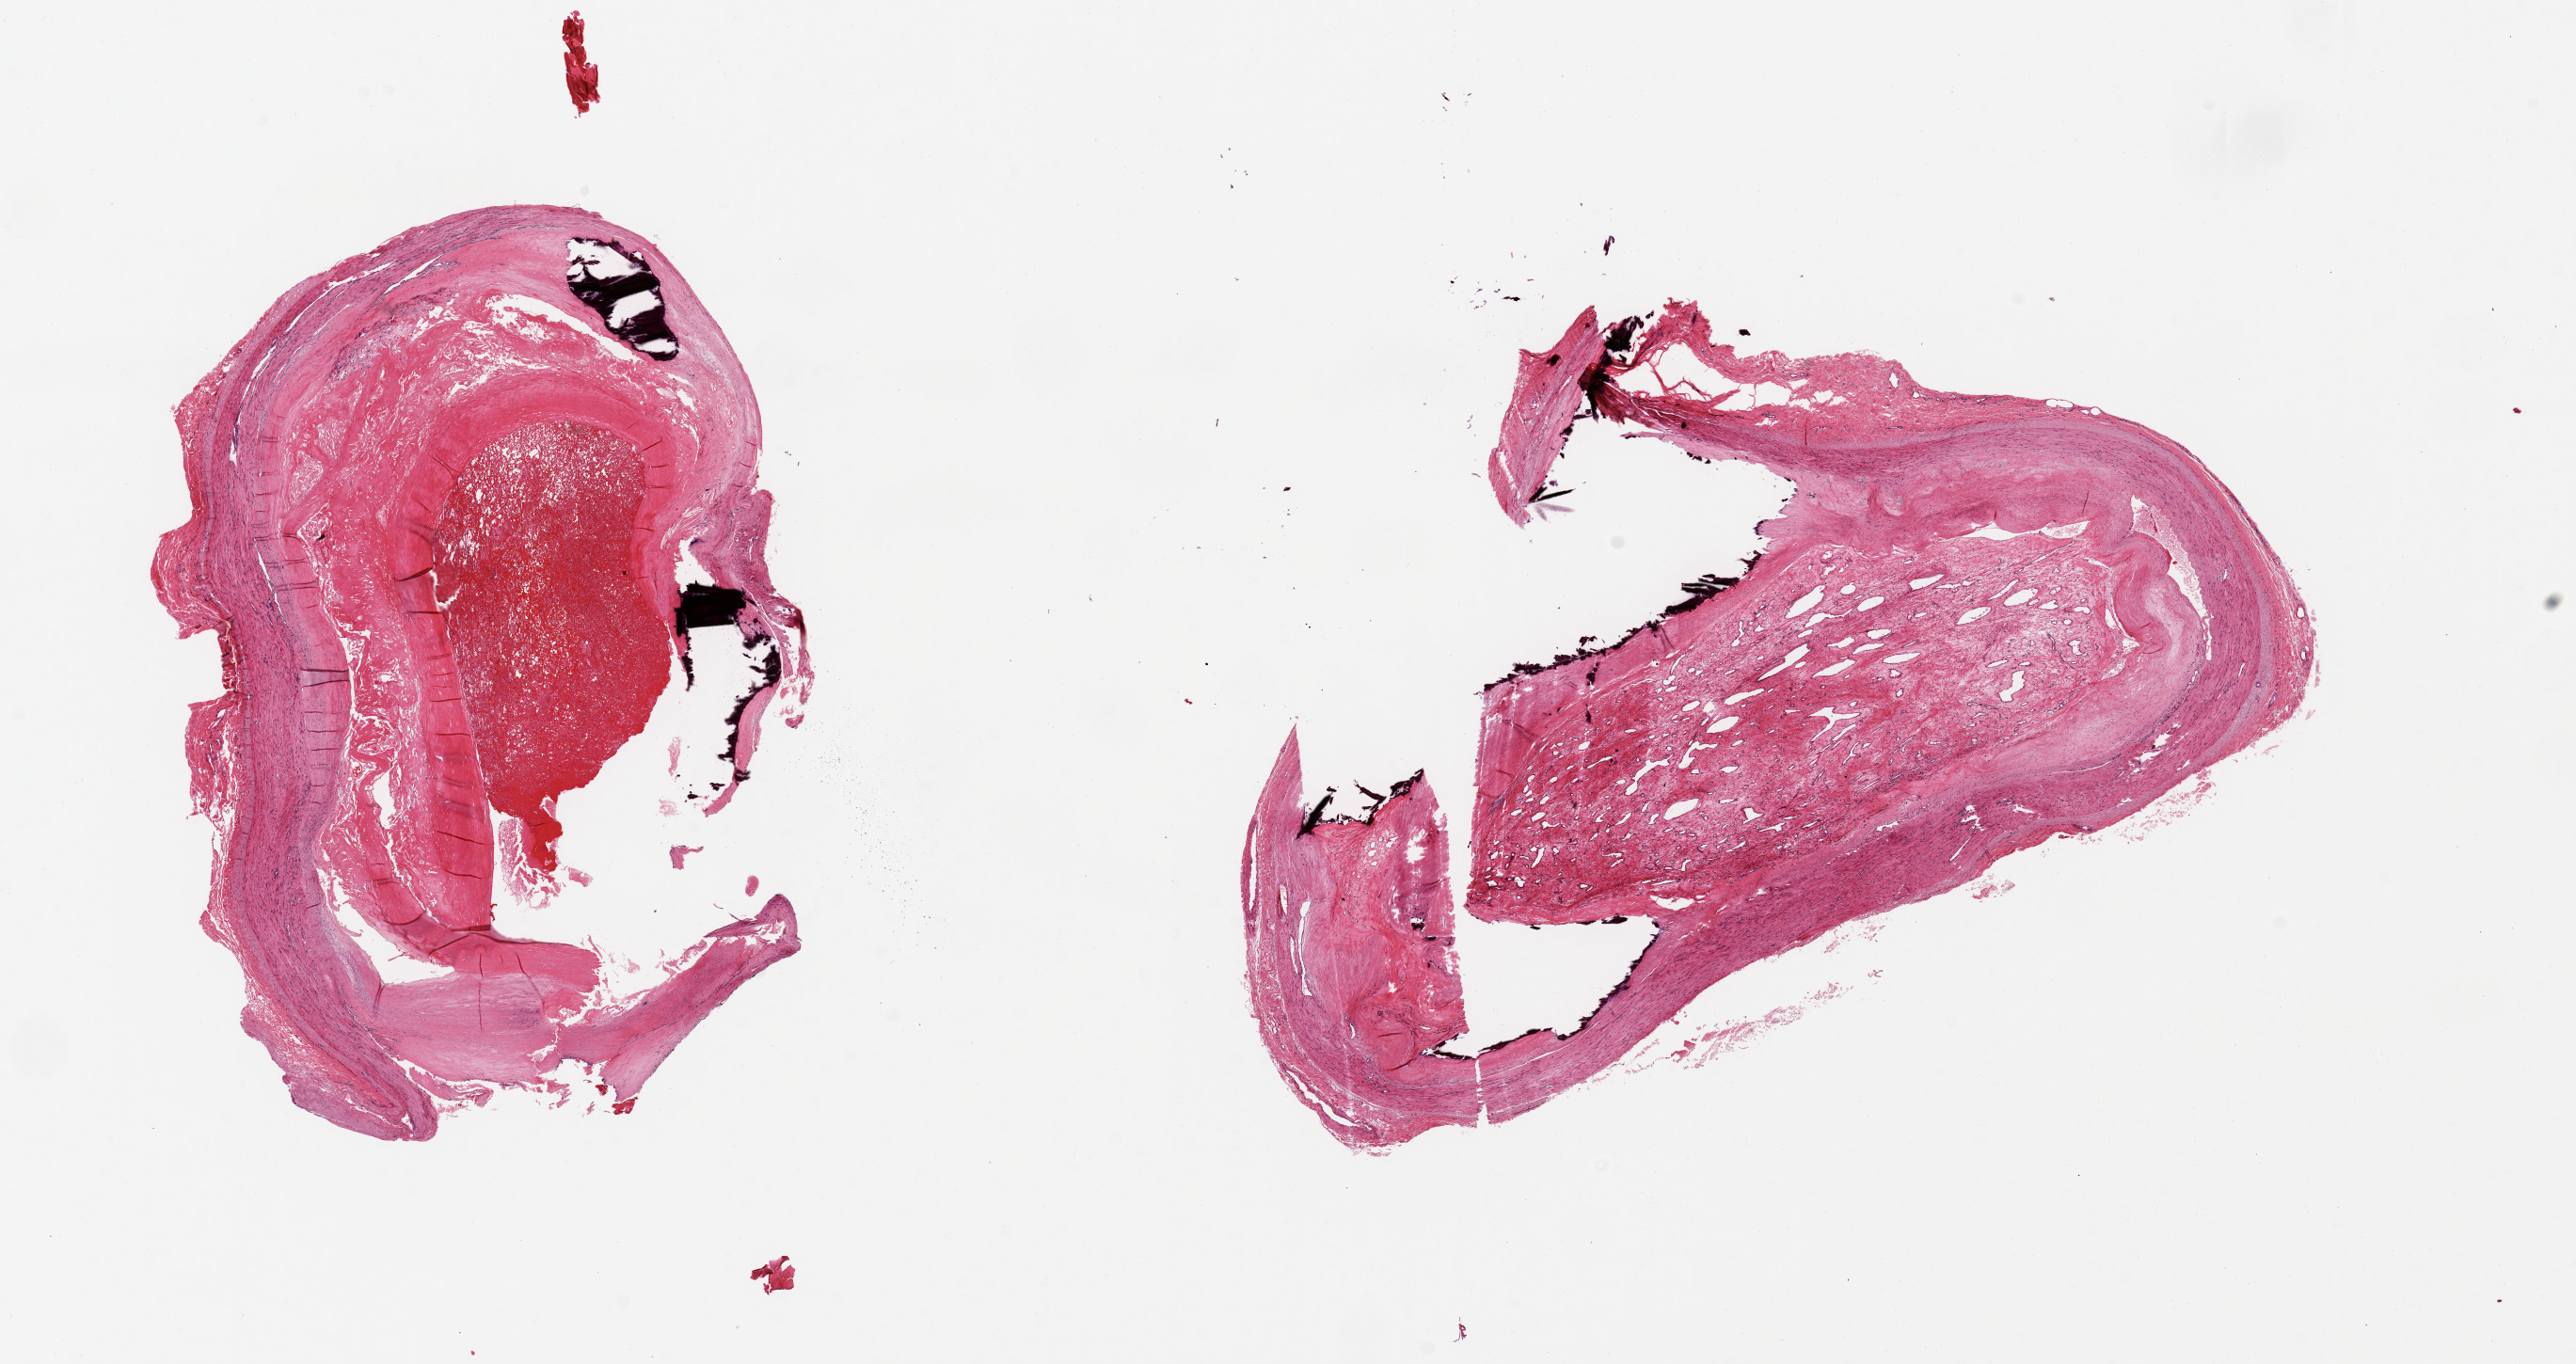
Whole-slide image, H&E stain — low-resolution overview of the scanned area, about 21.7 x 11.5 mm; PAXgene-fixed, paraffin-embedded tissue; sampled site (target tissue): tibial artery; donor tissue sample. Donor: male.
Pathologist's review note for this sample: 2 pieces 9x4 & 8x5 mm; Organized recanalized thrombus occupies entire lumen and ~50% of aliquot; calcium ~30%, little normal arterial wall in one aliquot; other has little normal wall as well with large recent thrombus and mural calcium. No patent lumen in either. (See photo).